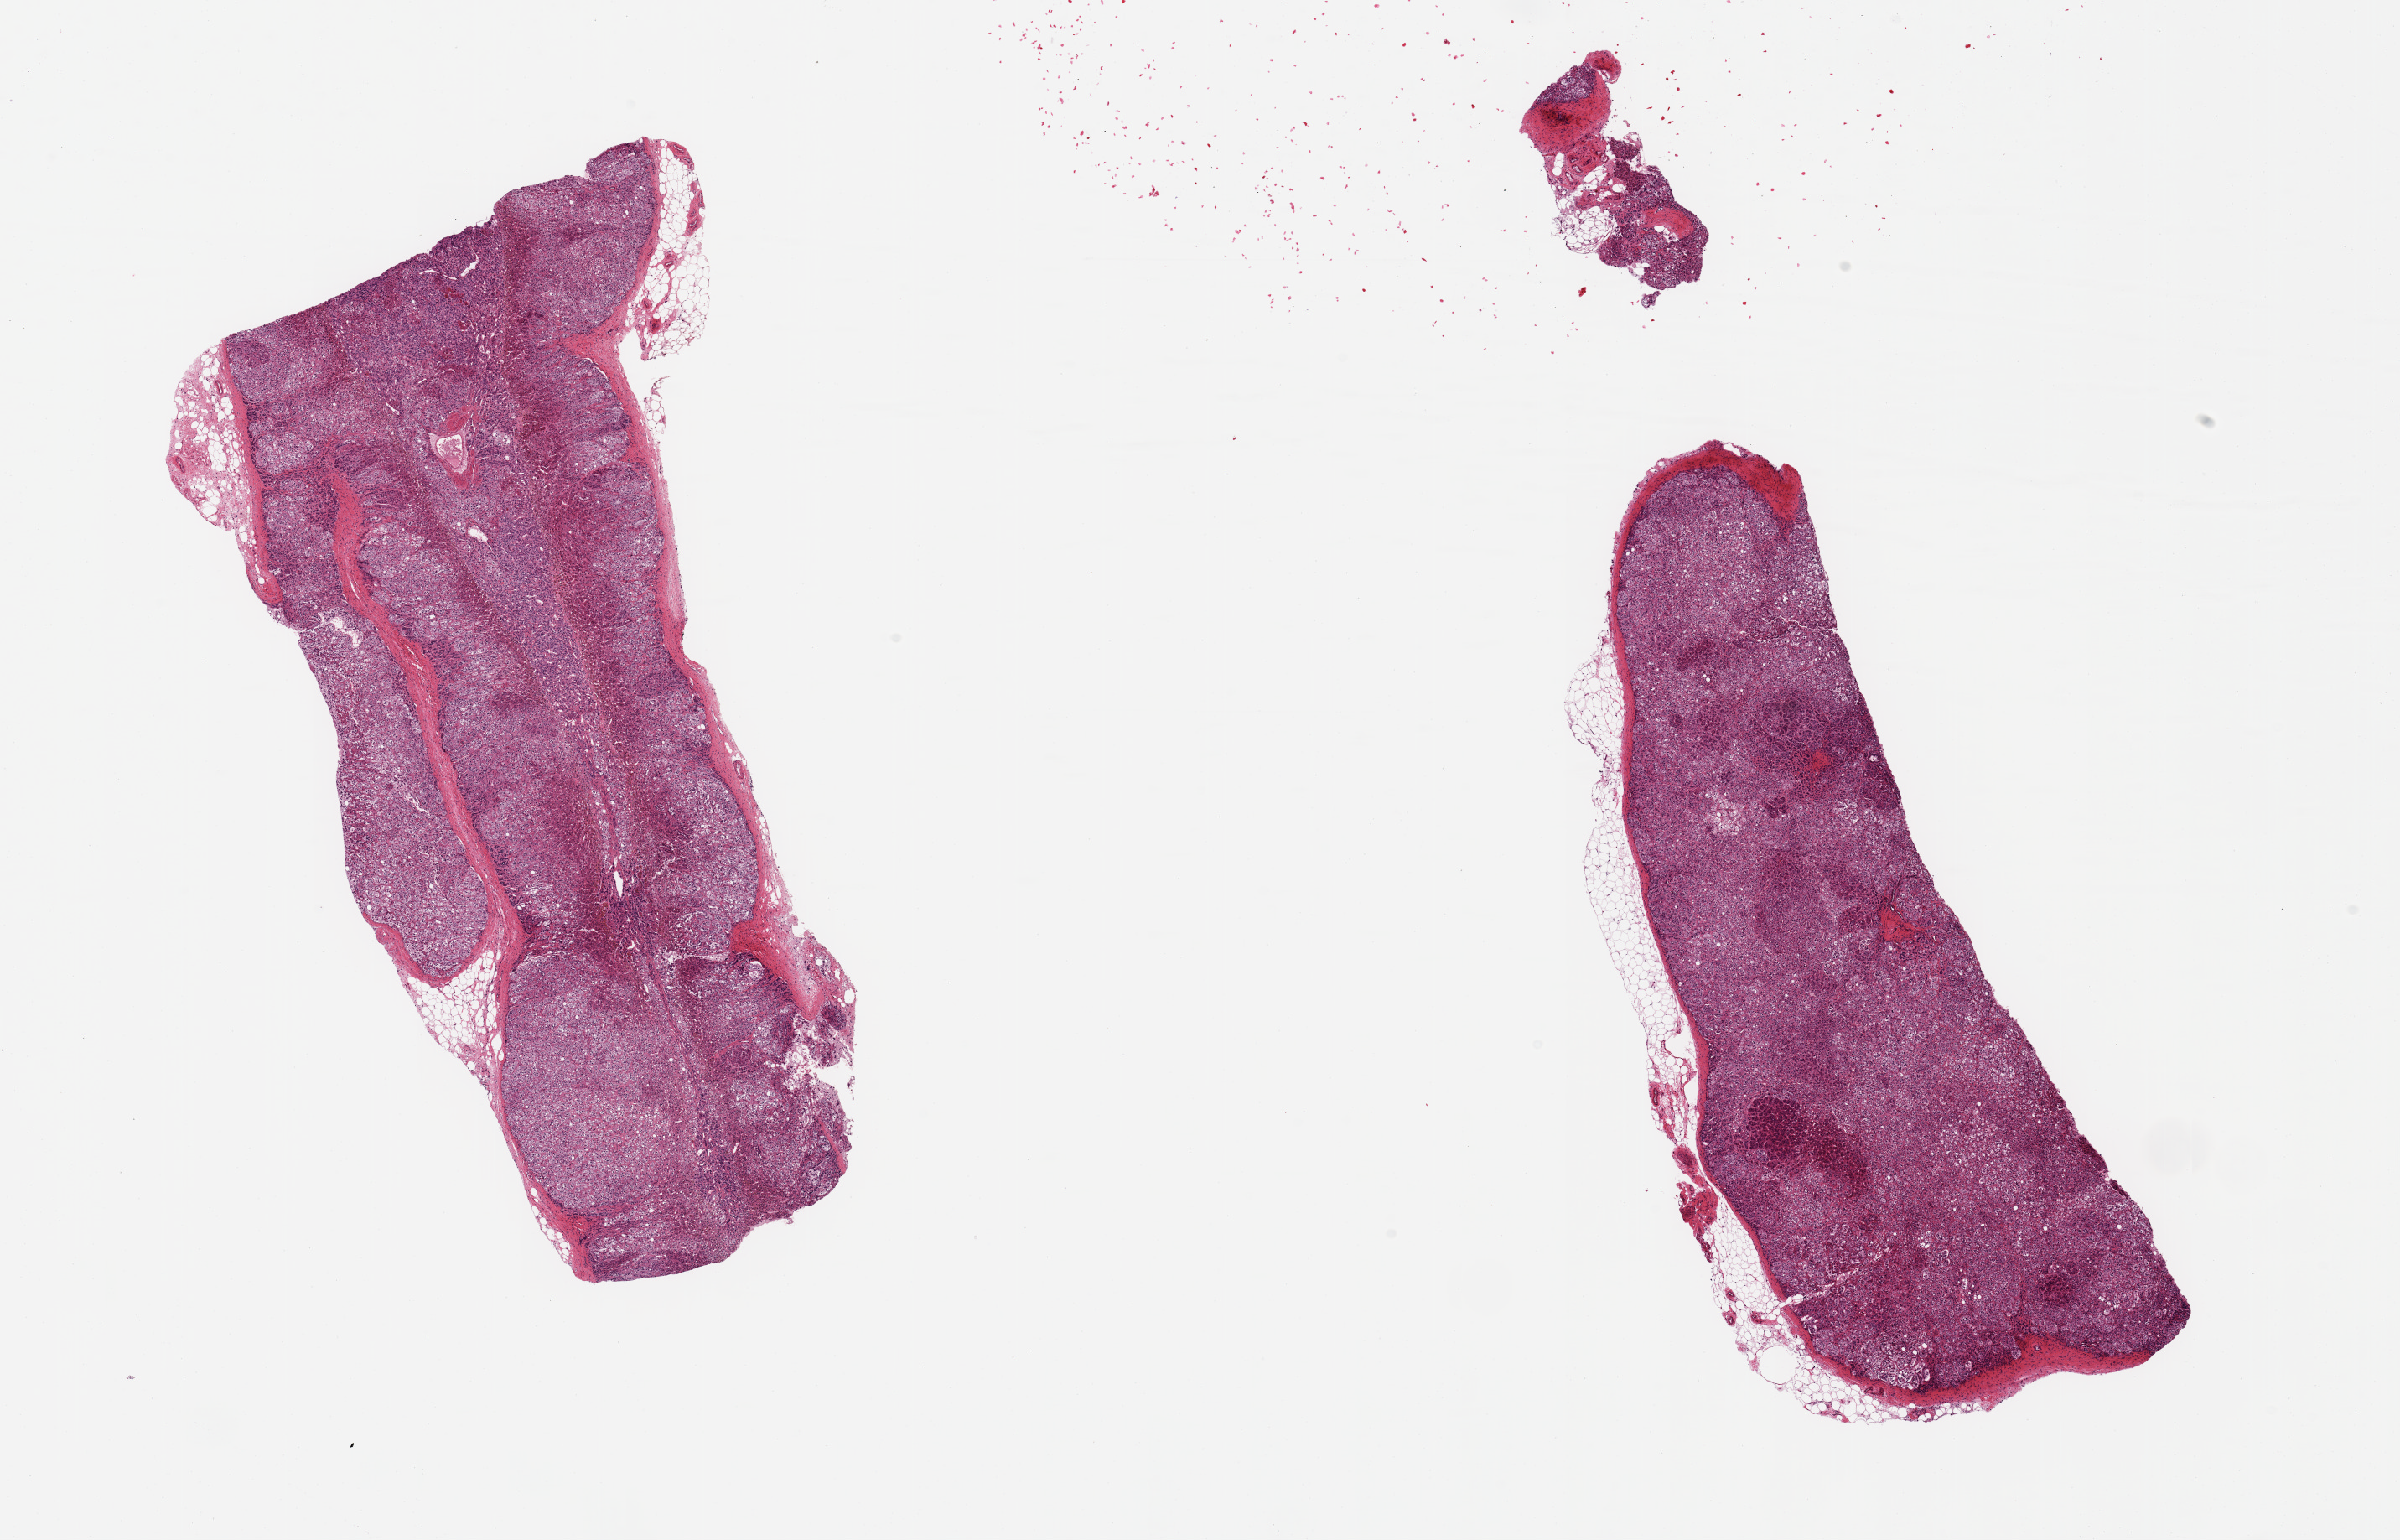
Haematoxylin and eosin whole-slide image — a low-resolution overview of the entire scanned area, about 22.6 x 14.5 mm (acquisition: 20x scan); PAXgene-fixed, paraffin-embedded tissue; sampled site (target tissue): adrenal gland; tissue donor sample. Donor sex: male.
Reviewer comment on this tissue sample: 2 pieces; well trimmed.